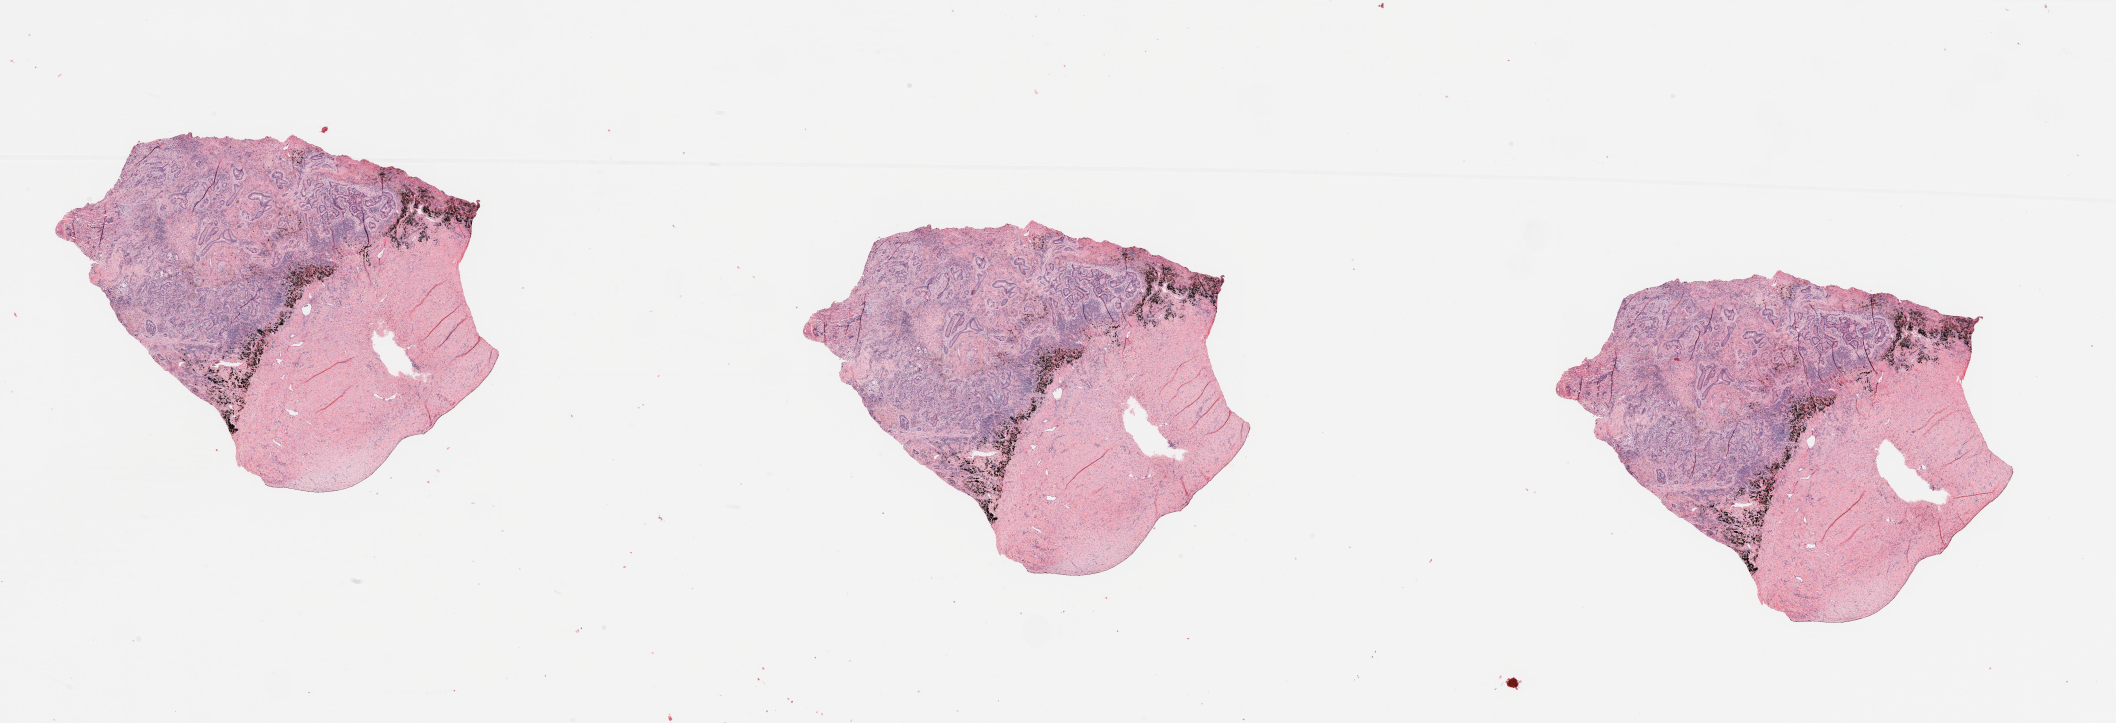
Digitized H&E-stained tissue section (whole slide), shown as a low-resolution overview of the whole scanned area (about 33.5 x 11.4 mm), tumour tissue sample, lung. Female, 70 y/o. Histologic grade: G1 (well differentiated).
• histologic diagnosis: Adenocarcinoma, NOS
• primary tumour site (as recorded): right upper lobe
• AJCC pathologic stage: IA